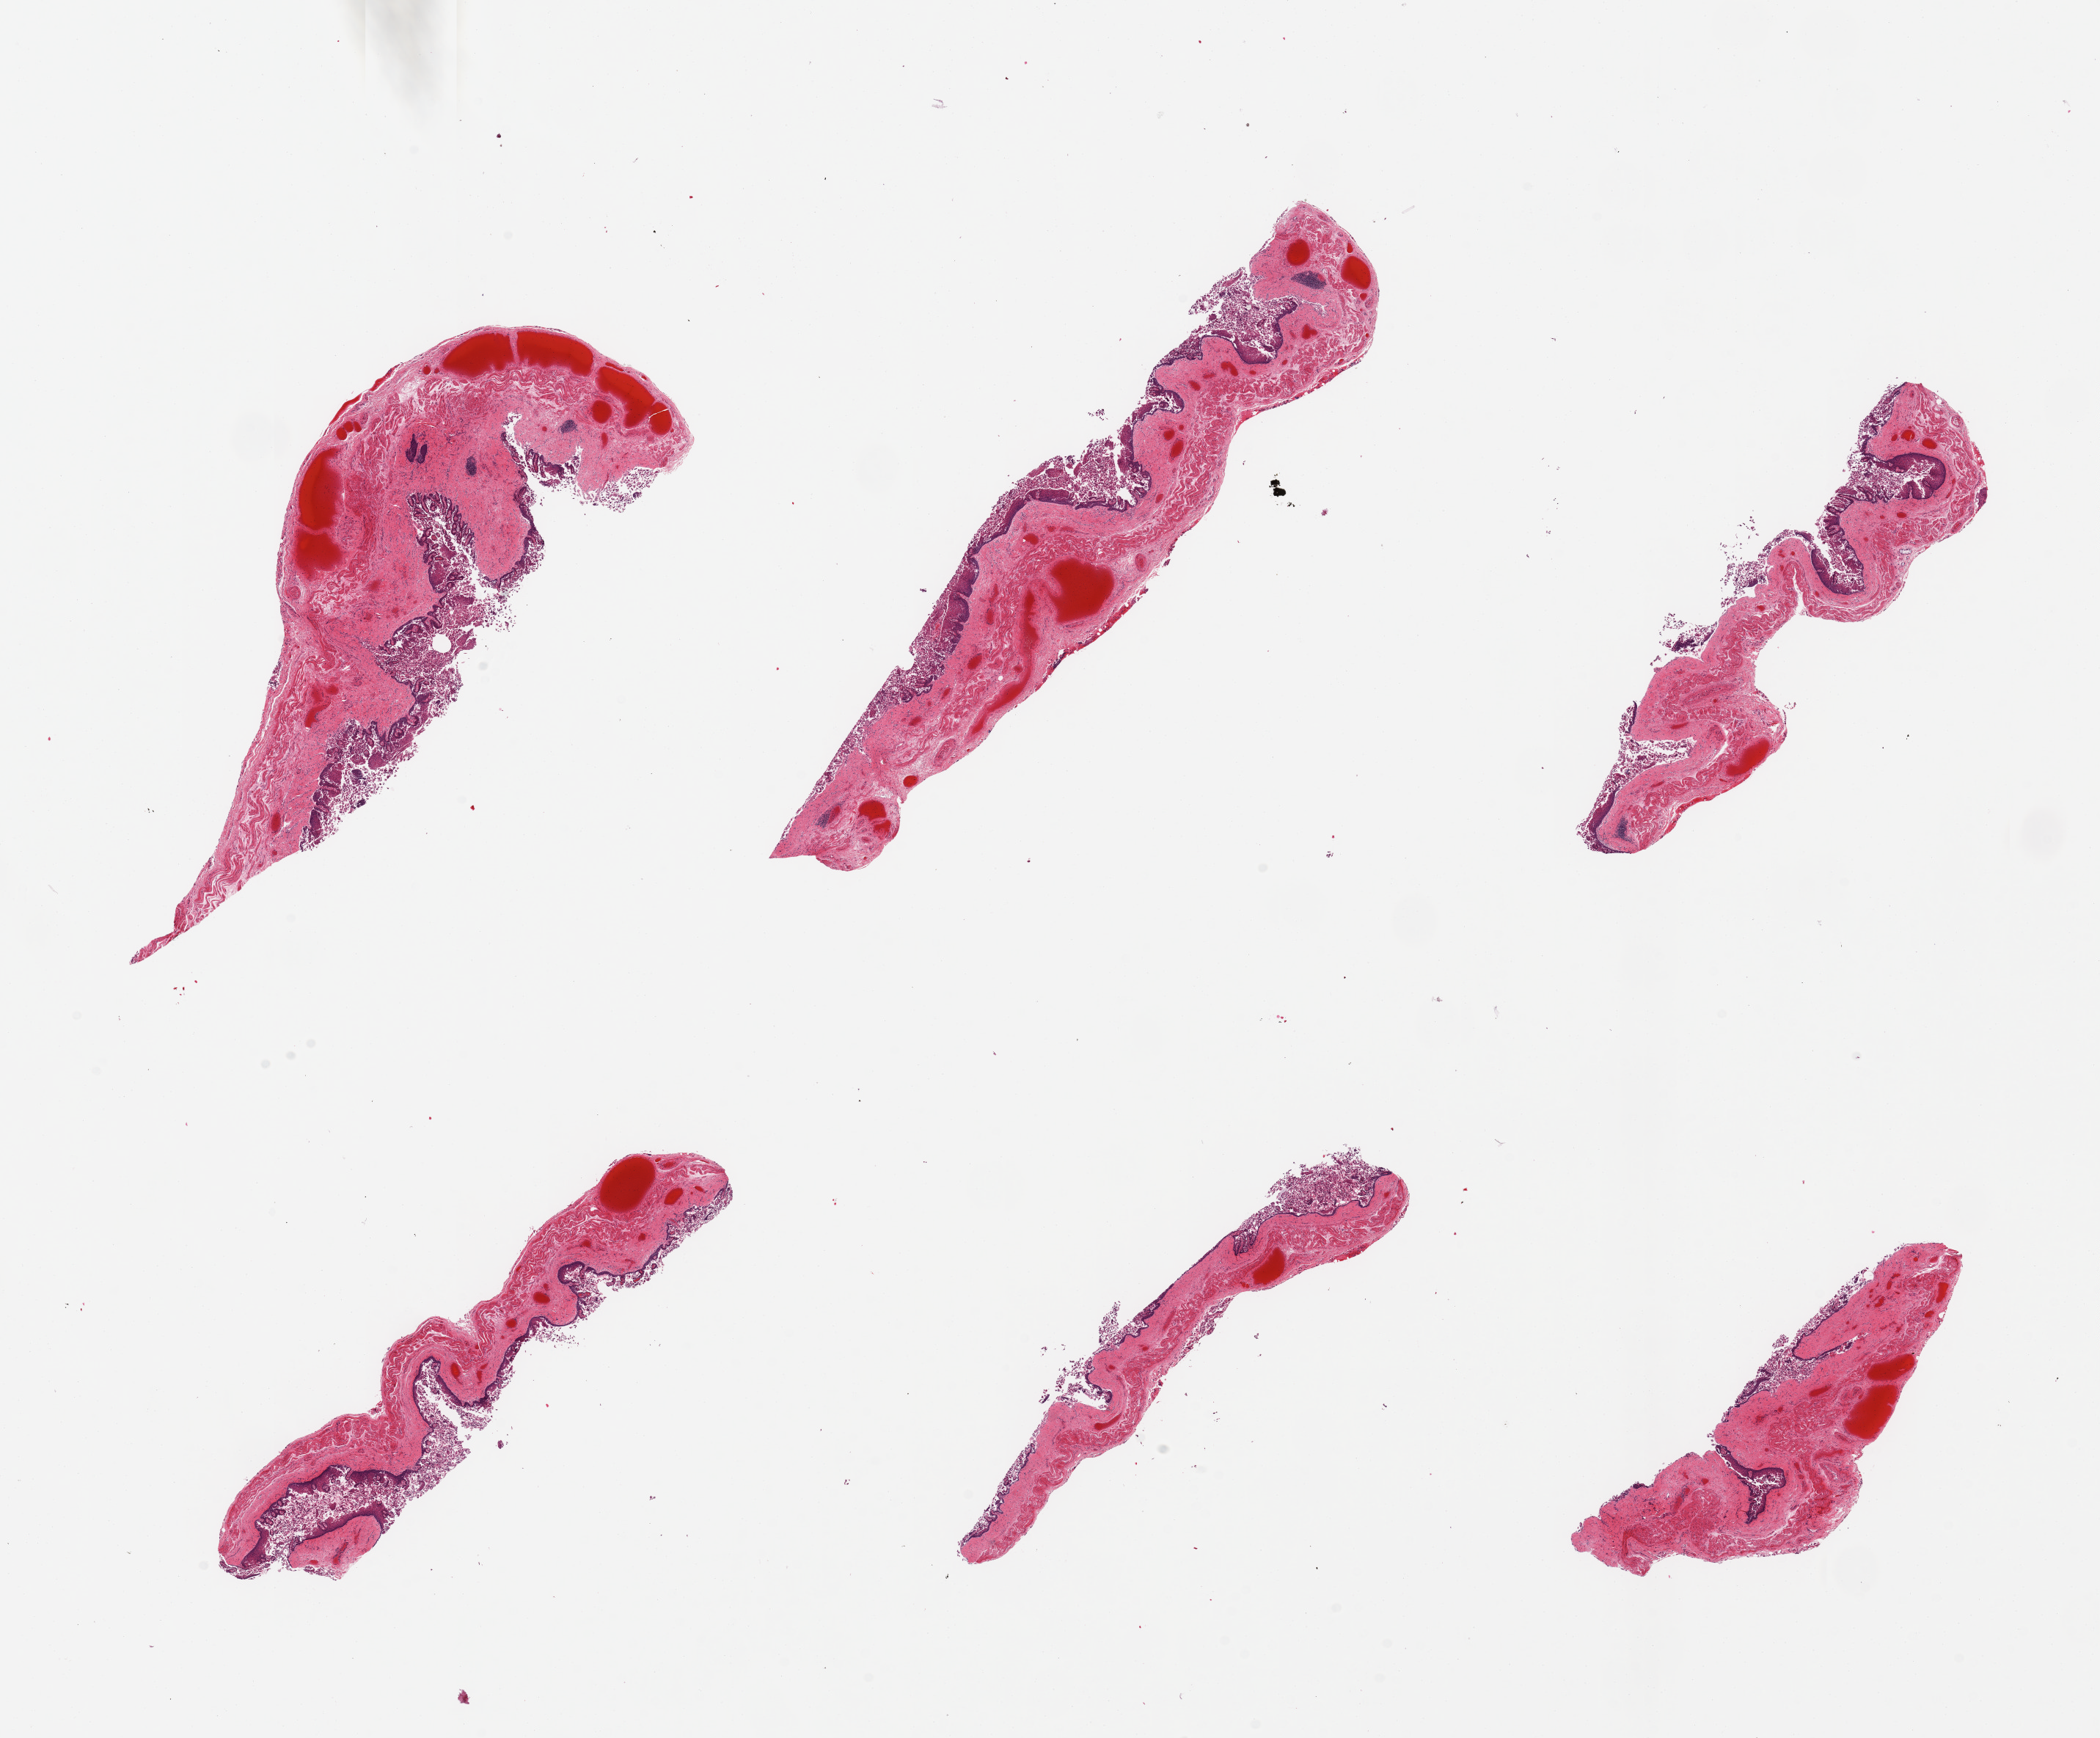
Whole-slide image, hematoxylin and eosin (H&E) stain — a low-resolution overview of the entire scanned area, about 22.6 x 18.7 mm, PAXgene-fixed paraffin-embedded (PFPE) section, sampled site (target tissue): esophageal mucous membrane, tissue donor sample. Donor: male.
Pathologist's review note for this sample: 6 pieces, autolyzing sloughing mucosa.